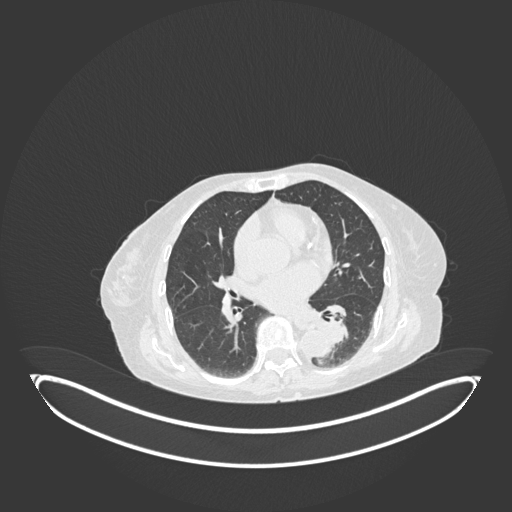
Chest CT, one axial slice. Position 56 of 189 along the scan axis. Reconstruction kernel B30f. 120 kVp. Lung window (W 1500 / L -600 HU). 512 × 512 image matrix, field of view 500 × 500 mm. Female patient, age 82 years. Case-level facts recorded for this patient, not image findings: clinical TNM (as recorded): T1b N0 M1.
Annotated regions visible in this slice (rectangle marked by the reading radiologist):
- lung tumour (recorded histology: adenocarcinoma): box from (x=311, y=310) to (x=357, y=351) px